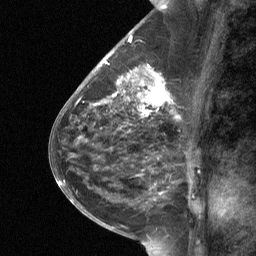
Breast MRI (dynamic contrast-enhanced), one sagittal slice; slice 28 of 64 in the series (ordered by position); dynamic contrast-enhanced study with each time point stored as its own series, time point 2 of 3 at this slice position (early post-contrast, ordered by acquisition time); 1.5 T; TE 4.8 ms, TR 27 ms; 256 × 256 image matrix. Patient: female, 59 years. From the clinical record (not read from this slice): setting: breast cancer imaged before/during neoadjuvant chemotherapy; receptor status: triple-negative.
Structures marked on this image (semi-automatic segmentation, software-assisted and operator-edited):
- analysis volume of interest (the breast-tissue region the enhancement analysis was run in; not a lesion): box from (x=113, y=66) to (x=171, y=120) px
- tumour enhancement mask (voxels above the 90 % enhancement threshold inside the analysis volume of interest): (x=113, y=68)–(x=168, y=106)